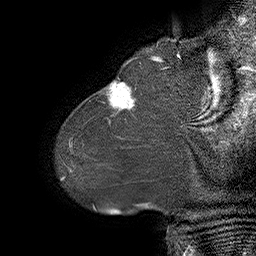
Breast MRI (dynamic contrast-enhanced), one sagittal slice. Slice 7 of 55 in the series (ordered by position). Dynamic contrast-enhanced series, time point 2 of 6 at this slice position (early post-contrast). 1.5 T. TE 4.5 ms, TR 32.4 ms. 3 mm slice thickness. 256 × 256 image matrix, field of view 180 × 180 mm. Female patient. From the clinical record (not read from this slice): setting: breast cancer imaged before/during neoadjuvant chemotherapy; receptor status: HER2-positive.
Outlined on this slice (semi-automatic segmentation, software-assisted and operator-edited):
- analysis volume of interest (the breast-tissue region the enhancement analysis was run in; not a lesion): box from (x=80, y=64) to (x=163, y=134) px
- tumour enhancement mask (voxels above the 100 % enhancement threshold inside the analysis volume of interest): (x=107, y=81)–(x=134, y=112)